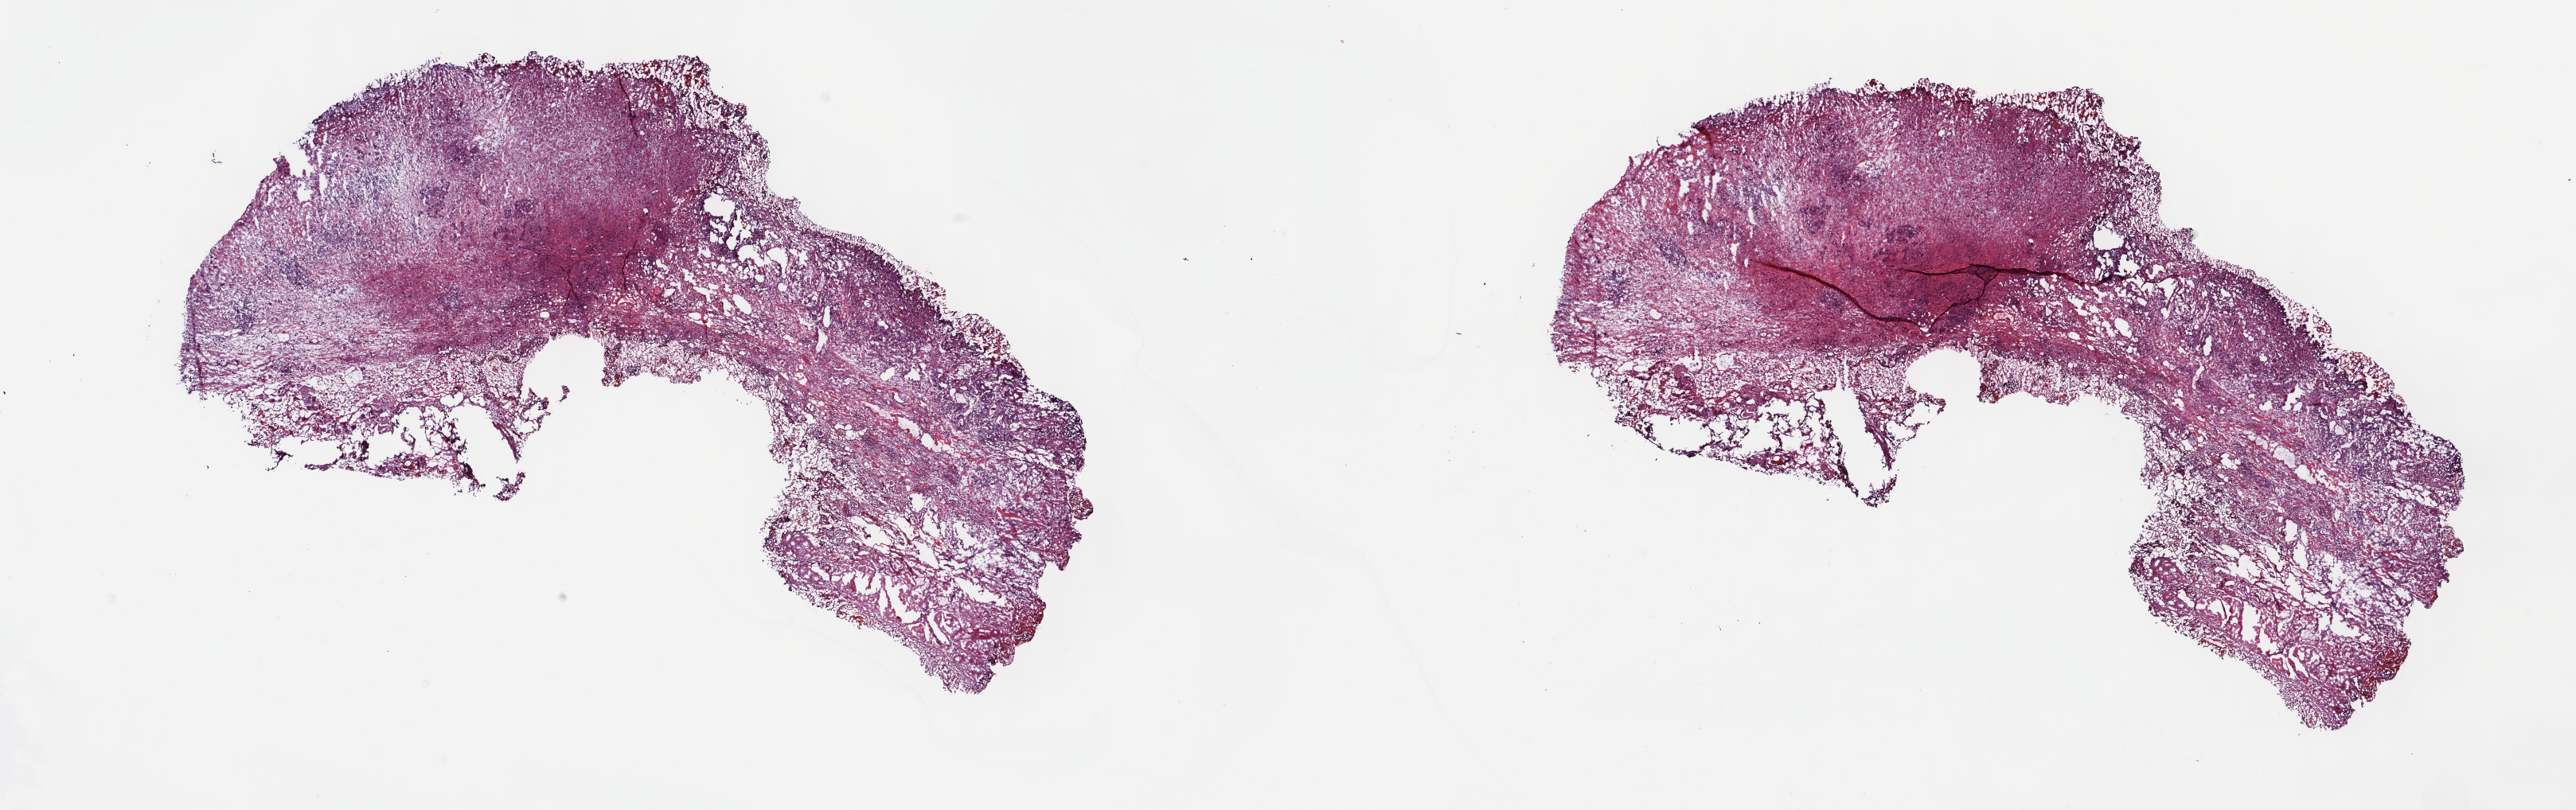
Digitized H&E tissue section (whole slide), shown as a low-resolution overview of the whole scanned area (about 26.2 x 8.2 mm, acquisition: 40x scan). Frozen section from the top of the tissue portion. Mesothelium, primary tumour sample. Male patient; age at initial diagnosis 58 years. Slide review estimates, as recorded: tumour cells 90%, tumour nuclei 65%, normal cells 0%, stromal cells 0%, necrosis 10%. Infiltration values recorded for this section: lymphocyte infiltration 3%, monocyte infiltration 0%, neutrophil infiltration 0%.
• histologic diagnosis: Epithelioid mesothelioma, malignant
• AJCC pathologic stage: III (6th edition)